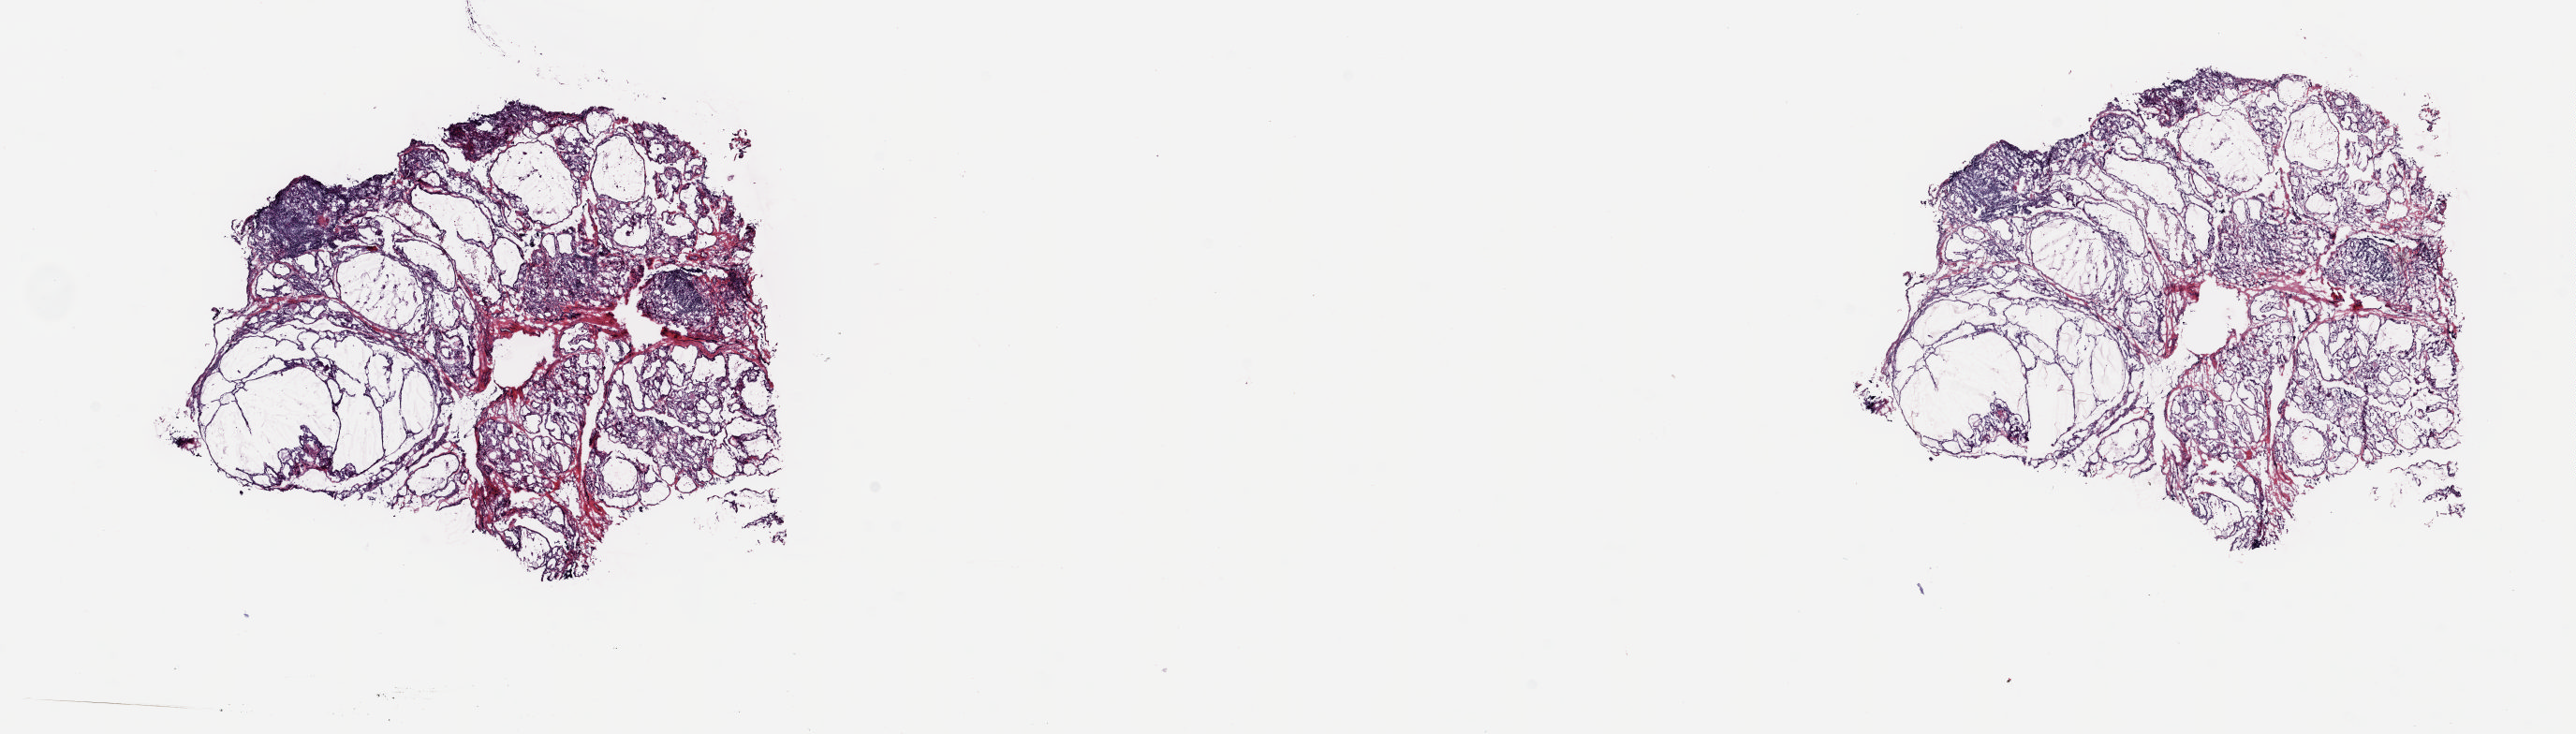
Digitized H&E tissue section (whole slide) — whole scanned area (about 21.8 x 6.2 mm) shown as a low-resolution overview; frozen section from the top of the tissue portion; thyroid, solid tissue normal (non-tumour tissue) sample. Male, age 33 years at initial diagnosis. Slide review estimates, as recorded: tumour cells 0%, tumour nuclei 0%, normal cells 95%, stromal cells 5%, necrosis 0%. Infiltration values recorded for this section: lymphocyte infiltration 10%, monocyte infiltration 1%, neutrophil infiltration 0%.
• this section: solid tissue normal (non-tumour) sample from the same patient
• patient diagnosis: Papillary carcinoma, follicular variant (thyroid gland)